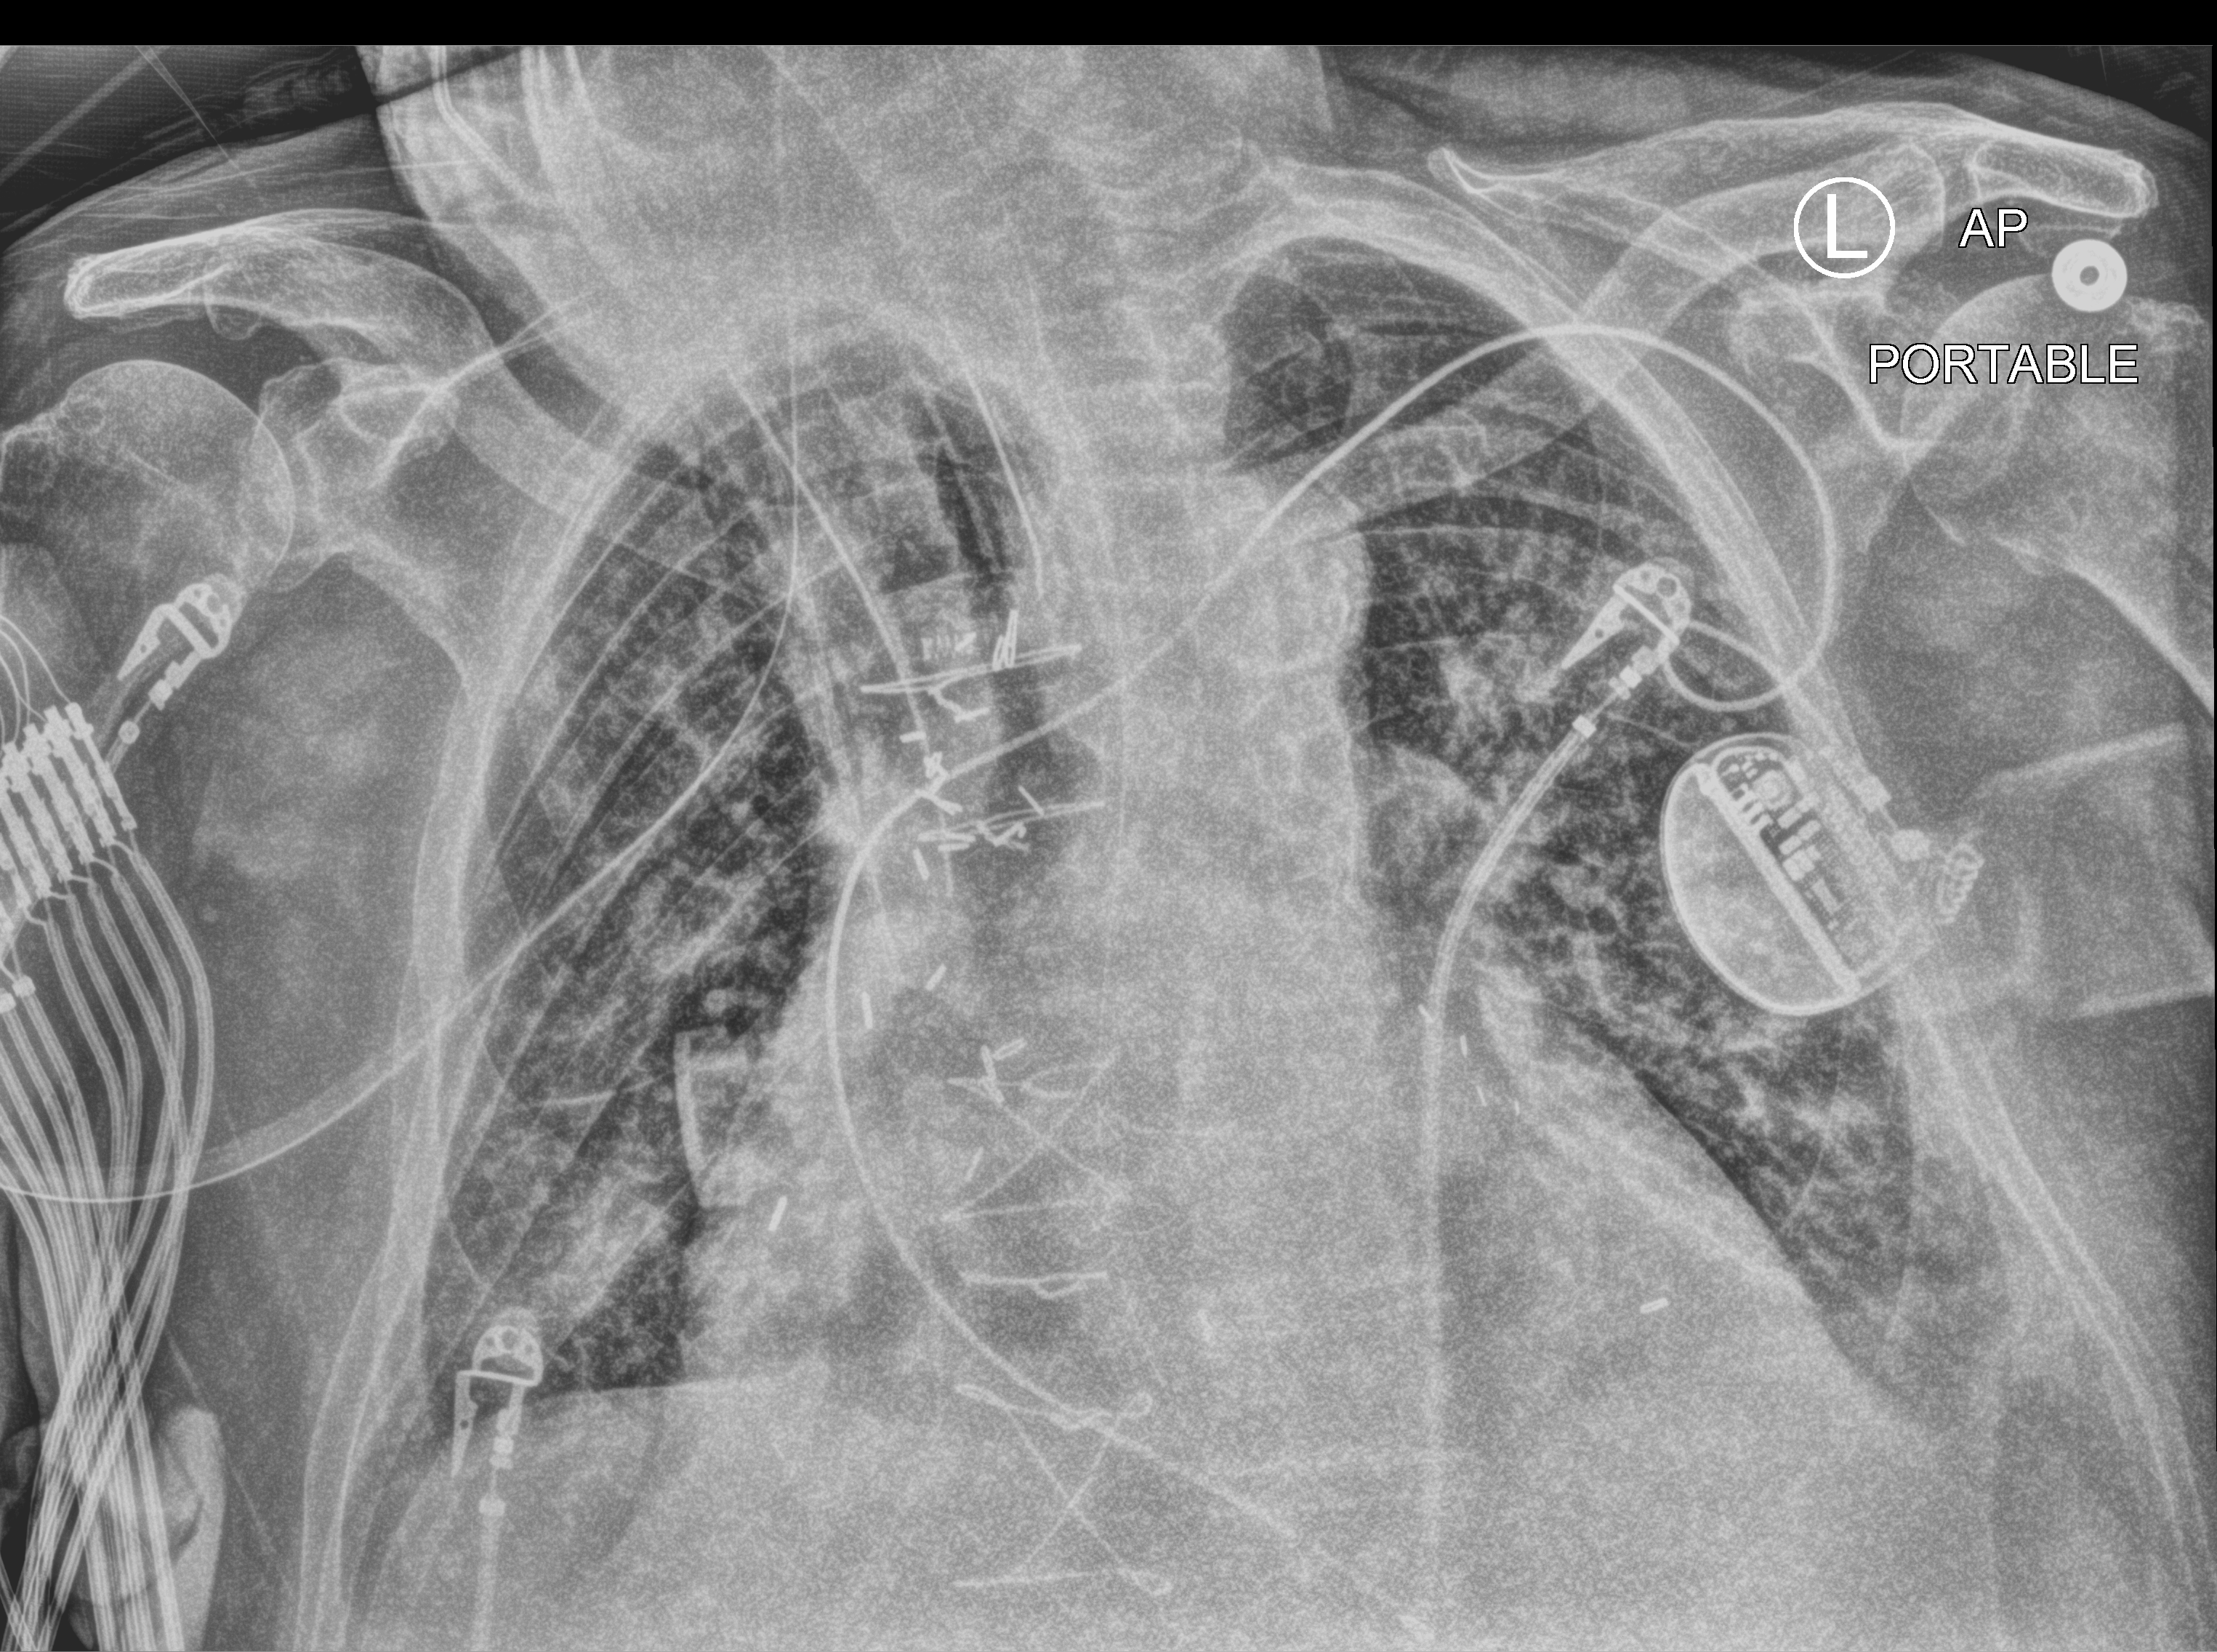
Portable chest radiograph; anteroposterior (AP) projection. Patient hospitalised with COVID-19; male, aged 75–90 years.
From the hospital-stay record, not from the radiograph (when in the stay this image was taken is not recorded):
- diabetes (admission record): yes
- admitted to intensive care during this hospital stay: yes
- mechanically ventilated during this hospital stay: yes